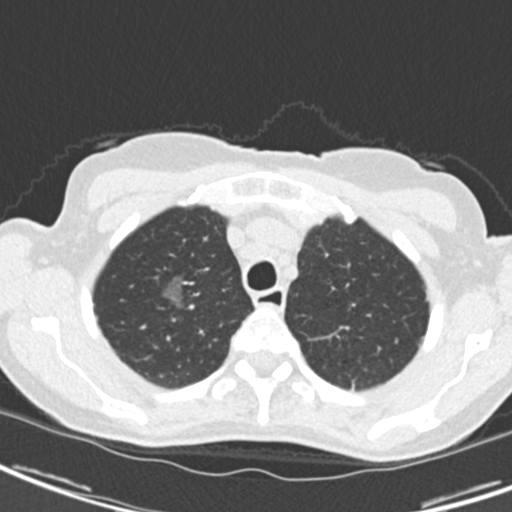
Low-dose screening chest CT, one axial slice. Slice 163 of 189 in the series (ordered by position). Reconstruction kernel B30f. Lung window (W 1500 / L -600 HU). 2 mm slice thickness. 512 × 512 image matrix.
Structures marked on this image (outlined manually by an expert reader):
- lesion 1 (tumor, upper lobe of right lung): bounding box <163,277,185,306> (left, top, right, bottom; pixels)